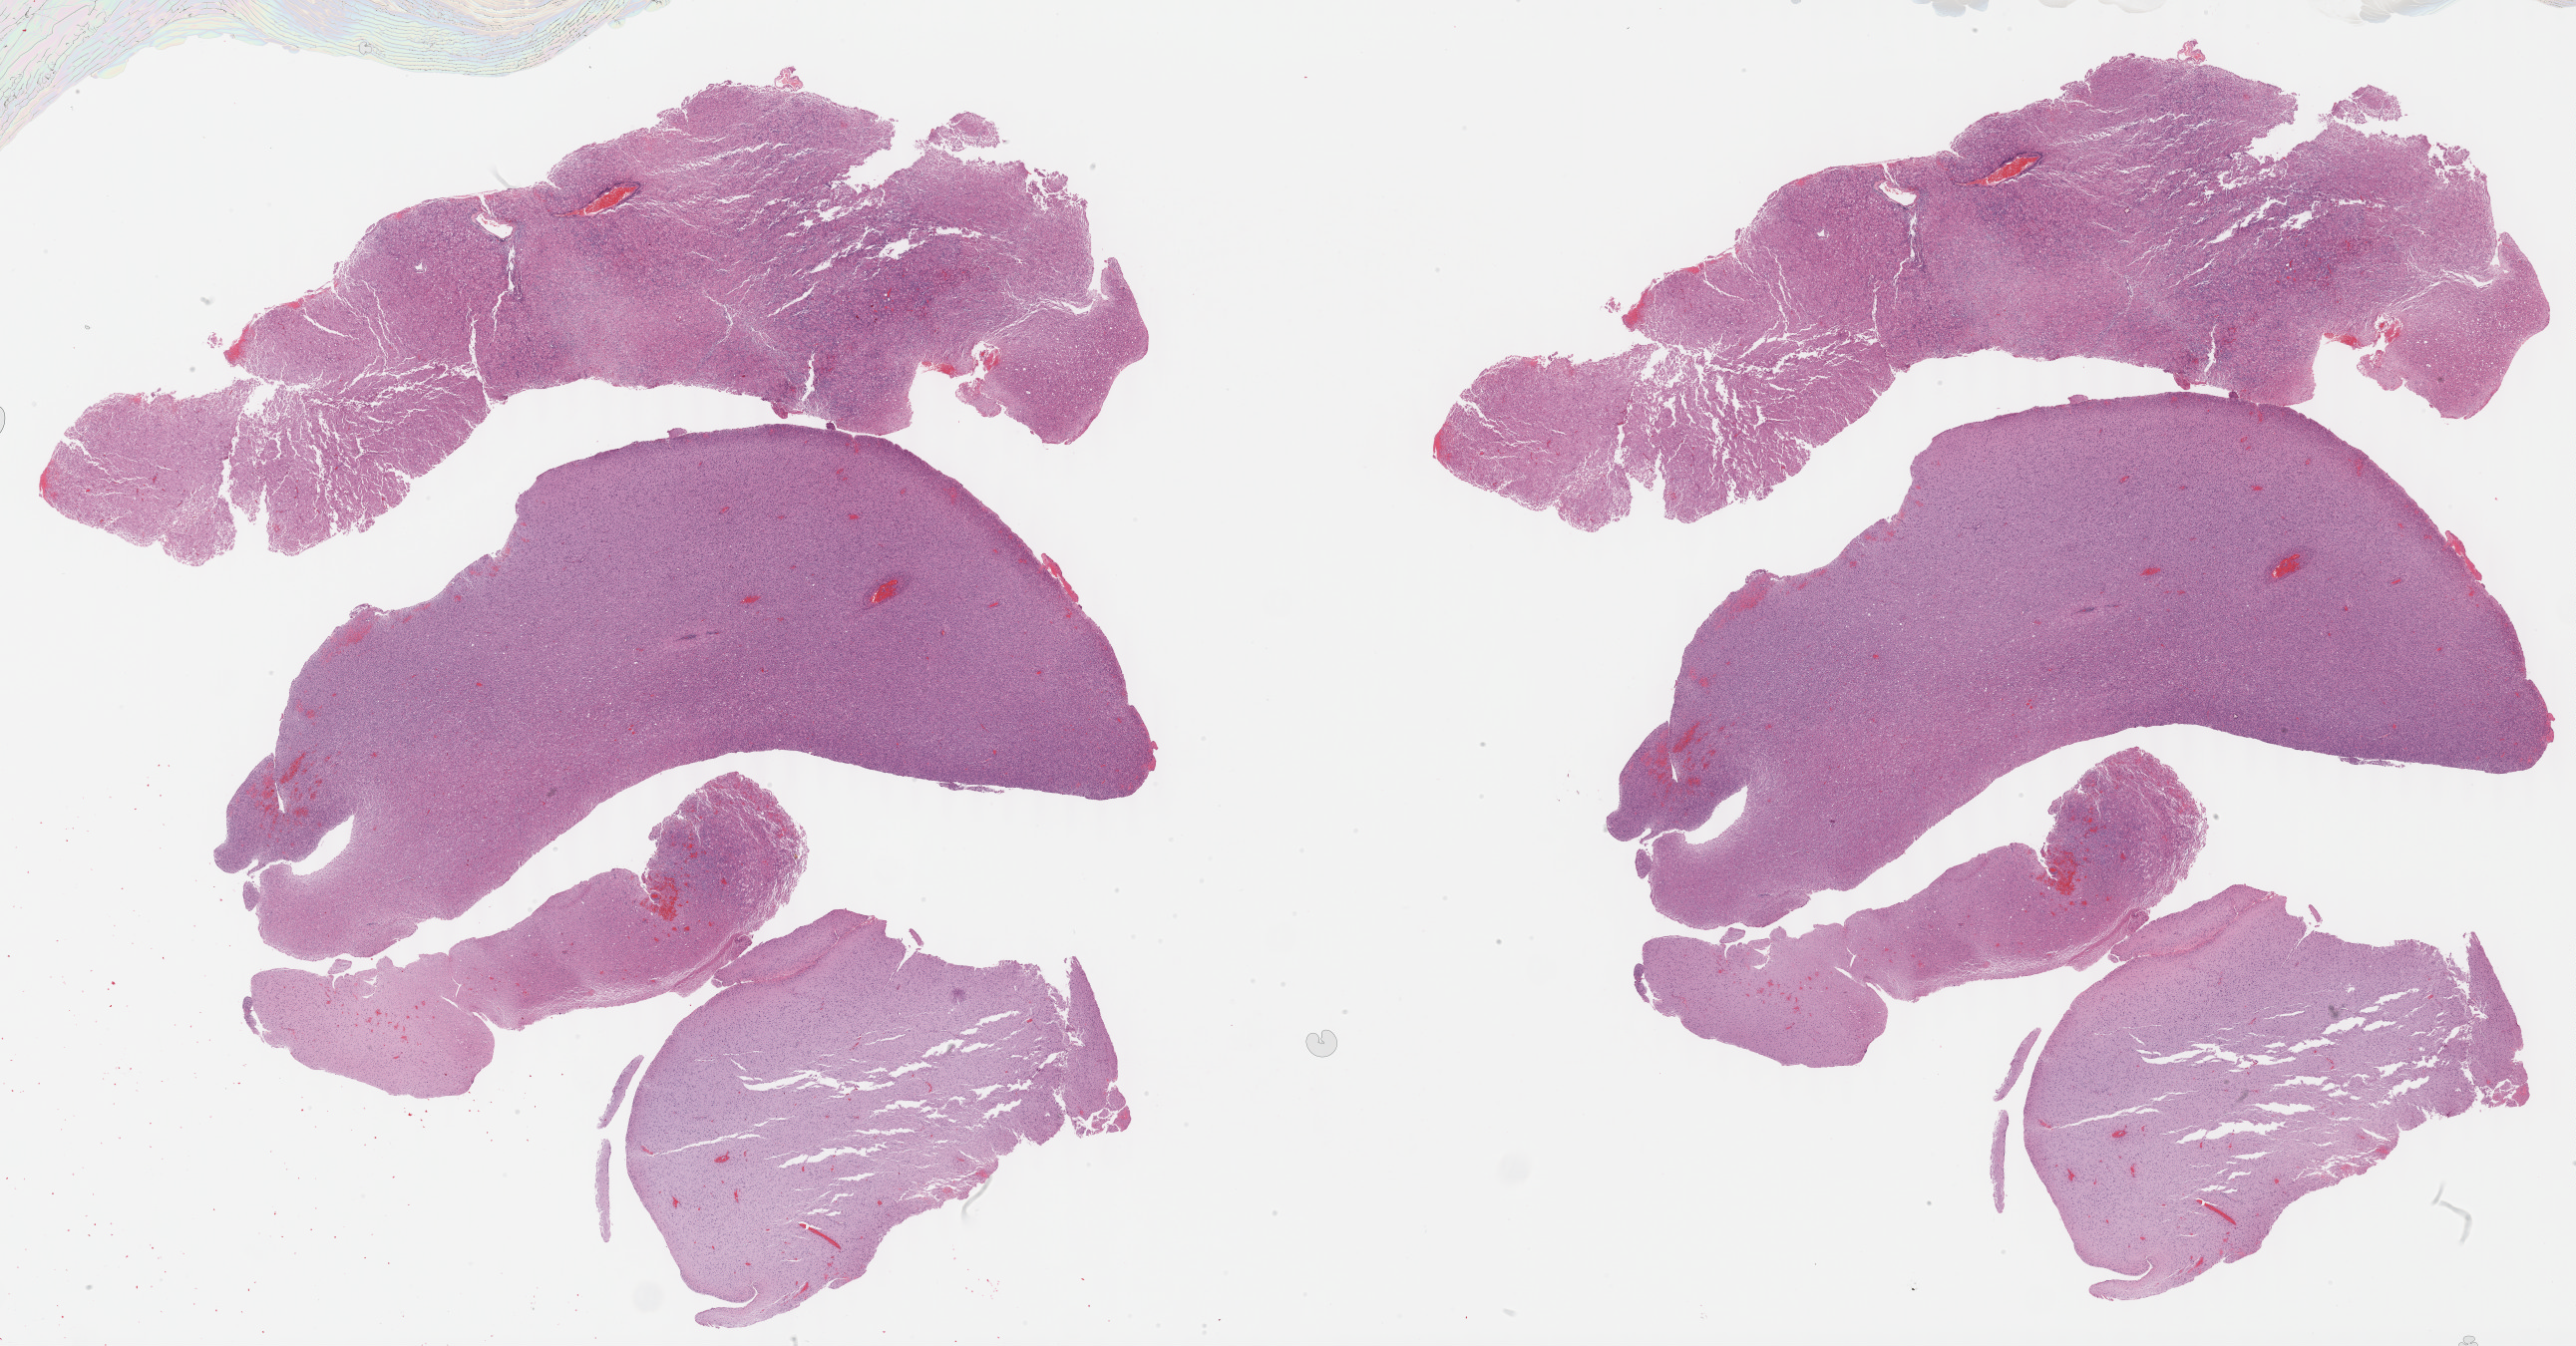
Whole-slide histology image, H&E-stained, whole scanned area (about 41.7 x 21.8 mm, from a 40x scan) shown as a low-resolution overview, formalin-fixed paraffin-embedded (FFPE) diagnostic section, sample: primary tumour, brain. Patient: male, age at initial diagnosis 55 years. Histologic grade: G3 (poorly differentiated).
Laterality: right. Diagnosis: Astrocytoma, anaplastic (cerebrum).